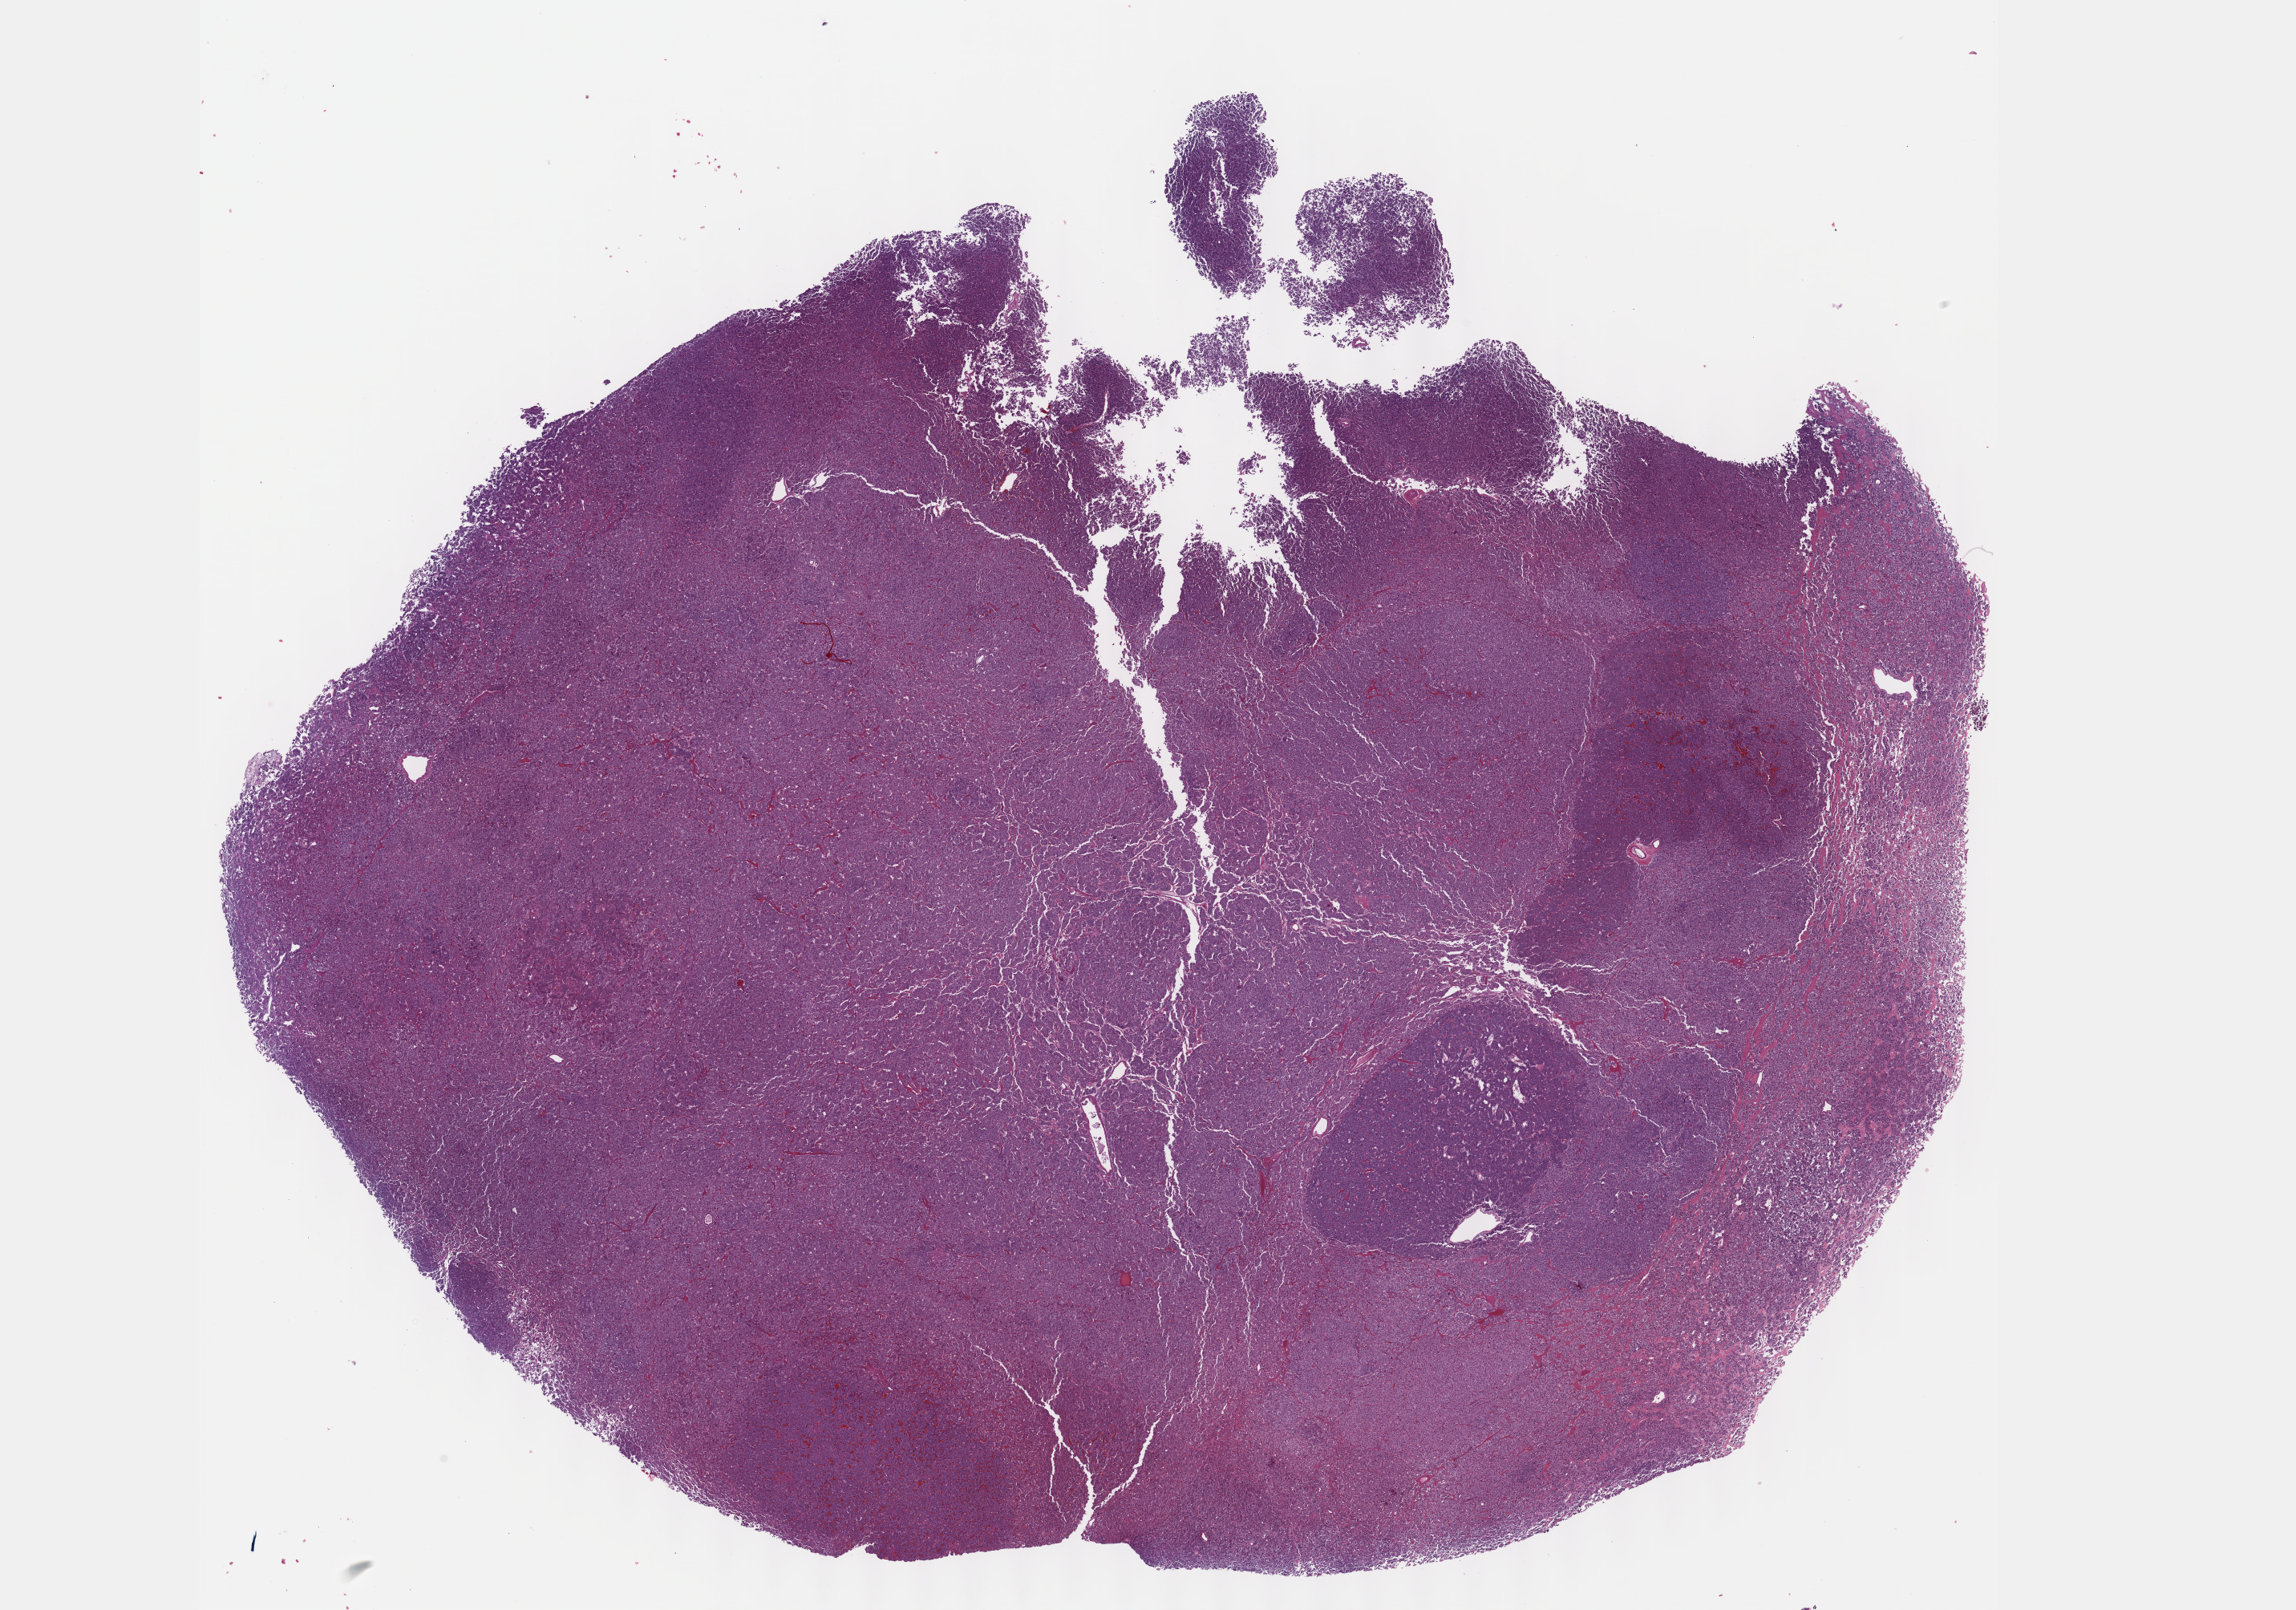
Whole-slide histology image, H&E, a low-resolution overview of the entire scanned area, about 23.1 x 16.2 mm (acquisition: 40x scan). FFPE section. Sample: primary tumour, adrenal gland. Female patient; age at initial diagnosis 46 years.
• pathologic diagnosis: Pheochromocytoma, NOS